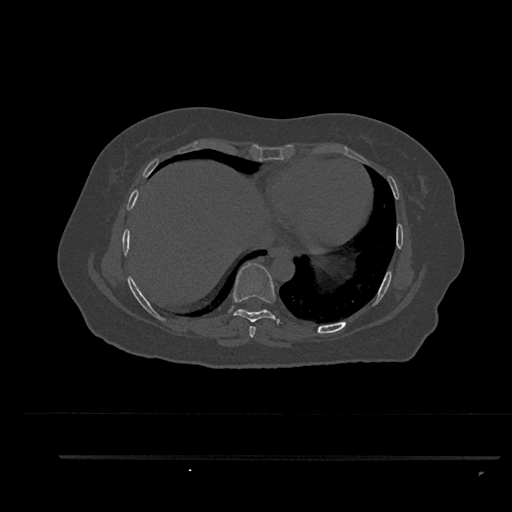
CT including the spine, one axial slice; position 457 of 797 along the scan axis; 120 kVp; bone window (W 1800 / L 400 HU); 512 × 512 image matrix. Patient: female, 44 years. Case-level facts recorded for this patient, not image findings: primary cancer: renal; vertebrae with lytic lesions (as recorded): L1.
Structures marked on this image (semi-automatically segmented with operator editing):
- T7 vertebra: box from (x=249, y=326) to (x=256, y=338) px
- T8 vertebra: (x=233, y=262)–(x=282, y=325)